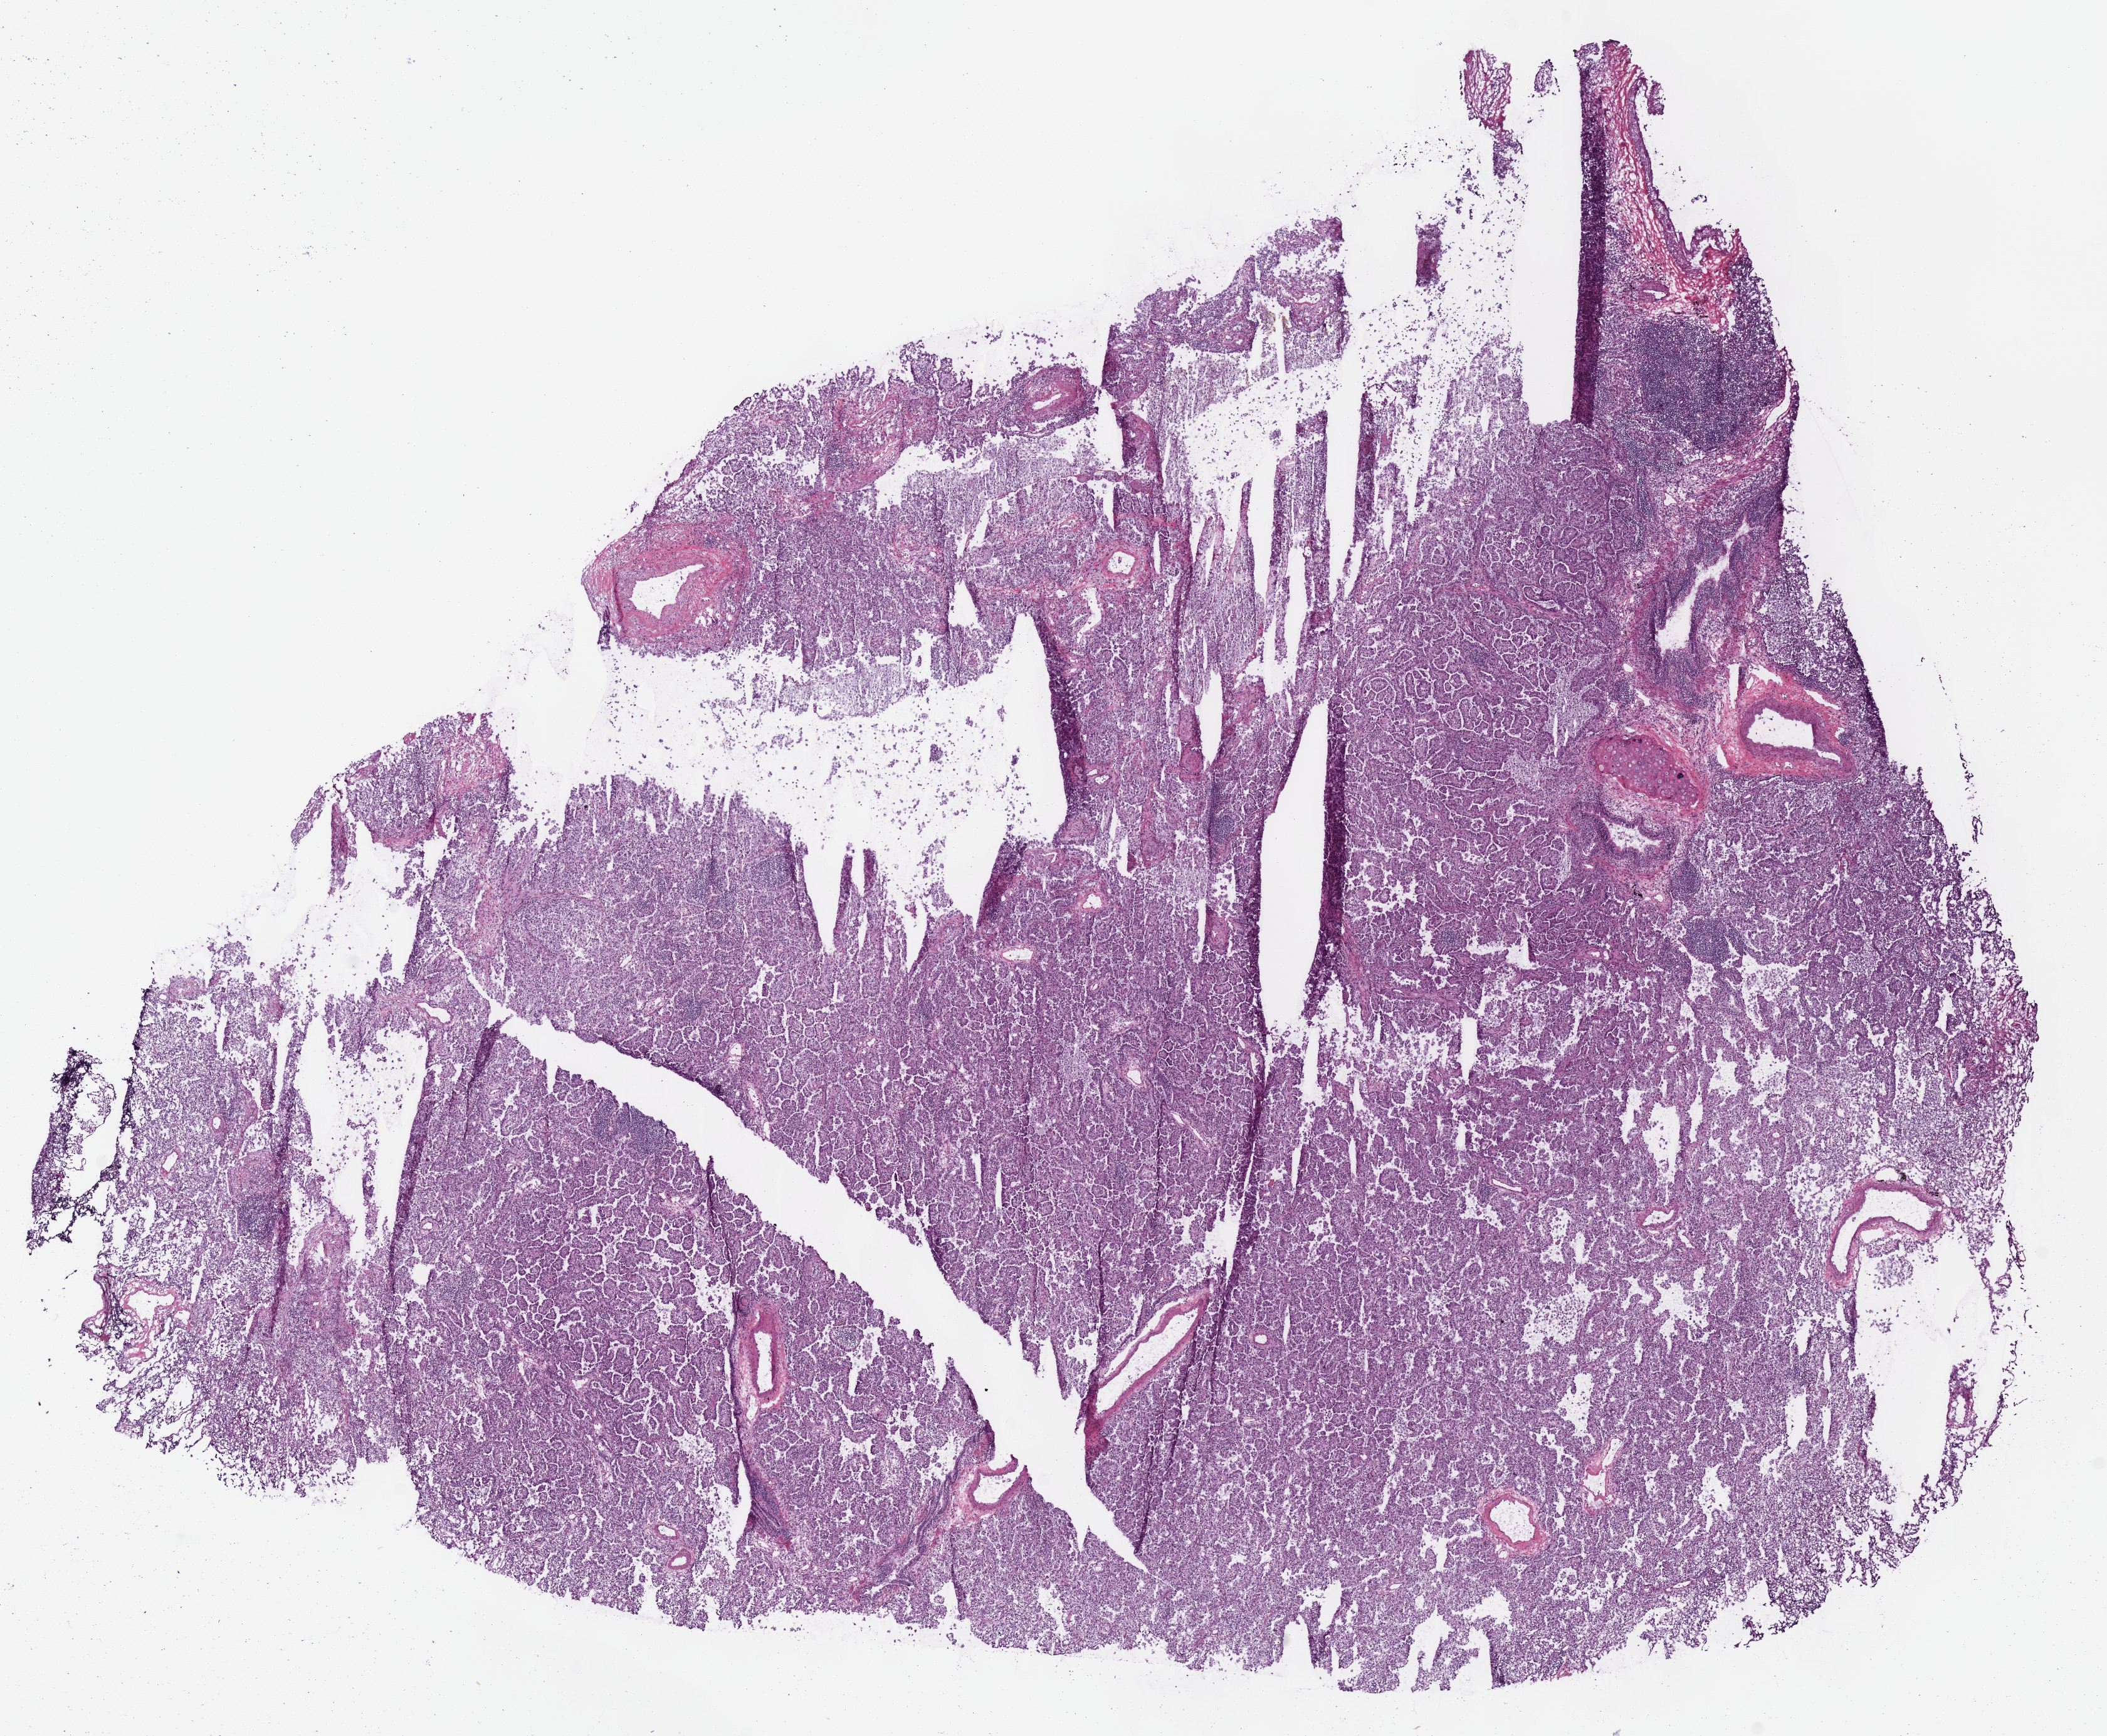
H&E-stained whole-slide image — shown as a low-resolution overview of the whole scanned area (about 13.2 x 10.9 mm, acquisition: 40x scan). Frozen section from the top of the tissue portion. Lung, primary tumour sample. Patient: female, age at initial diagnosis 63 years. Slide review estimates, as recorded: tumour cells 85%, tumour nuclei 85%, normal cells 4%, stromal cells 6%, necrosis 5%. Infiltration values recorded for this section: lymphocyte infiltration 7%.
• AJCC pathologic stage: IIIA (7th edition)
• TNM: T4 N0 M0
• histologic diagnosis: Adenocarcinoma with mixed subtypes (upper lobe, lung)